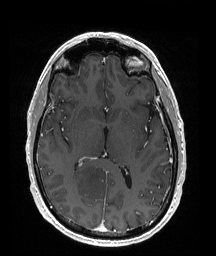
Brain MRI from a brain-tumour surgery series, one axial slice; position 94 of 176 along the scan axis; T1-weighted post-contrast; 216 × 256 image matrix, field of view 211 × 250 mm. Case-level facts recorded for this patient, not image findings: histopathology: Oligodendroglioma; WHO grade: 2; IDH mutation: yes.
Annotated regions visible in this slice (manually delineated by an expert):
- tumour: bounding box (x1, y1, x2, y2) in pixels: (70, 161, 111, 198)